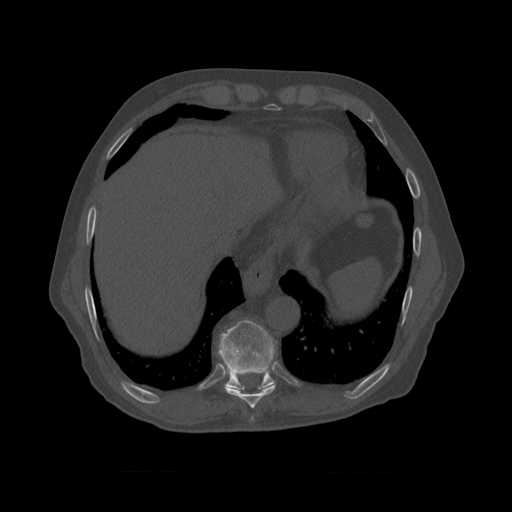
CT including the spine, one axial slice; slice 437 of 450 in the series (ordered by position); reconstruction kernel STANDARD; 120 kVp; bone window (W 1800 / L 400 HU); 1.25 mm slice thickness; 512 × 512 image matrix. Patient age 75 years. Case-level facts recorded for this patient, not image findings: primary cancer: prostate.
Outlined on this slice (semi-automatically segmented with operator editing):
- T8 vertebra: bounding box (x1, y1, x2, y2) in pixels: (219, 334, 276, 409)
- T9 vertebra: (219, 320, 276, 389)